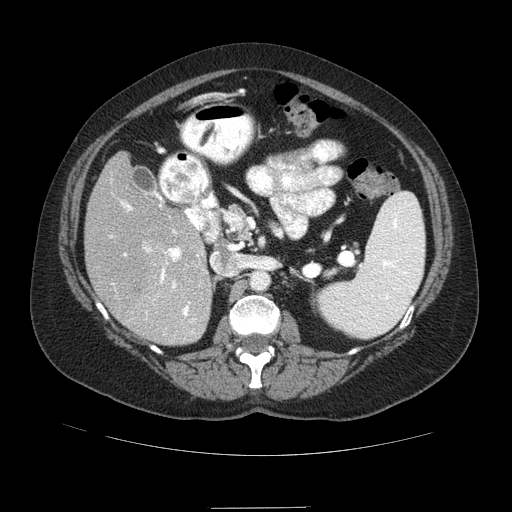
Contrast-enhanced abdominal CT (liver protocol), one axial slice. Position 40 of 89 along the scan axis. 120 kVp. Soft-tissue window (W 400 / L 40 HU). 512 × 512 image matrix. Case-level facts recorded for this patient, not image findings: diagnosis: hepatocellular carcinoma (patient treated with transarterial chemoembolisation; whether this scan precedes or follows treatment is not stated here); TNM stage (as recorded): Stage-IIIB; Child-Pugh class: A.
Structures marked on this image (semi-automatically segmented with operator editing):
- liver parenchyma outside the tumour (the mass and vessels are separate outlines, so this box may not span the whole liver): bounding box [x1, y1, x2, y2] px = [84, 152, 212, 344]
- mass: [130, 283, 141, 296]
- liver vessels: [110, 192, 198, 334]